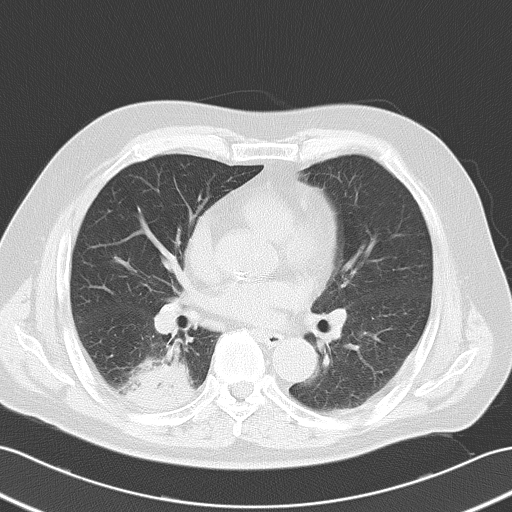
Chest CT, one axial slice. Slice 21 of 52 in the series (ordered by position). Reconstruction kernel B70f. 120 kVp. Lung window (W 1500 / L -600 HU). 512 × 512 image matrix, field of view 353 × 353 mm. Patient: male, 70 years. From the clinical record (not read from this slice): clinical TNM (as recorded): T2 N0 M0.
Annotated regions visible in this slice (bounding box drawn by a radiologist):
- lung tumour (recorded histology: adenocarcinoma): bounding box (x1, y1, x2, y2) in pixels: (124, 350, 200, 418)